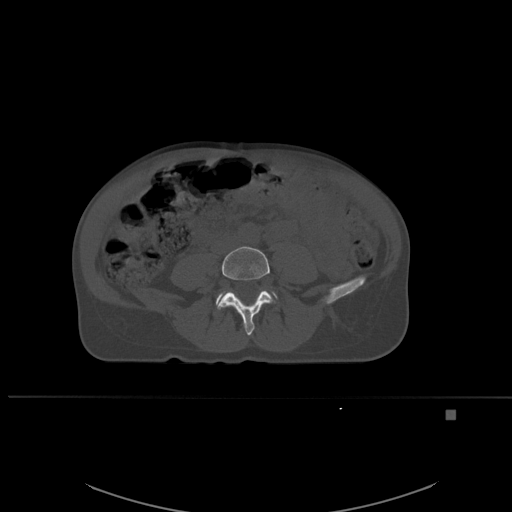
CT including the spine, one axial slice; position 188 of 537 along the scan axis; bone window (W 1800 / L 400 HU); 1.5 mm slice thickness; 512 × 512 image matrix, field of view 440 × 440 mm. Patient: female, 45 years. Case-level facts recorded for this patient, not image findings: primary cancer: lung.
Annotated regions visible in this slice (semi-automatic segmentation, software-assisted and operator-edited):
- L4 vertebra: box from (x=216, y=246) to (x=274, y=336) px
- L5 vertebra: (x=216, y=291)–(x=277, y=304)